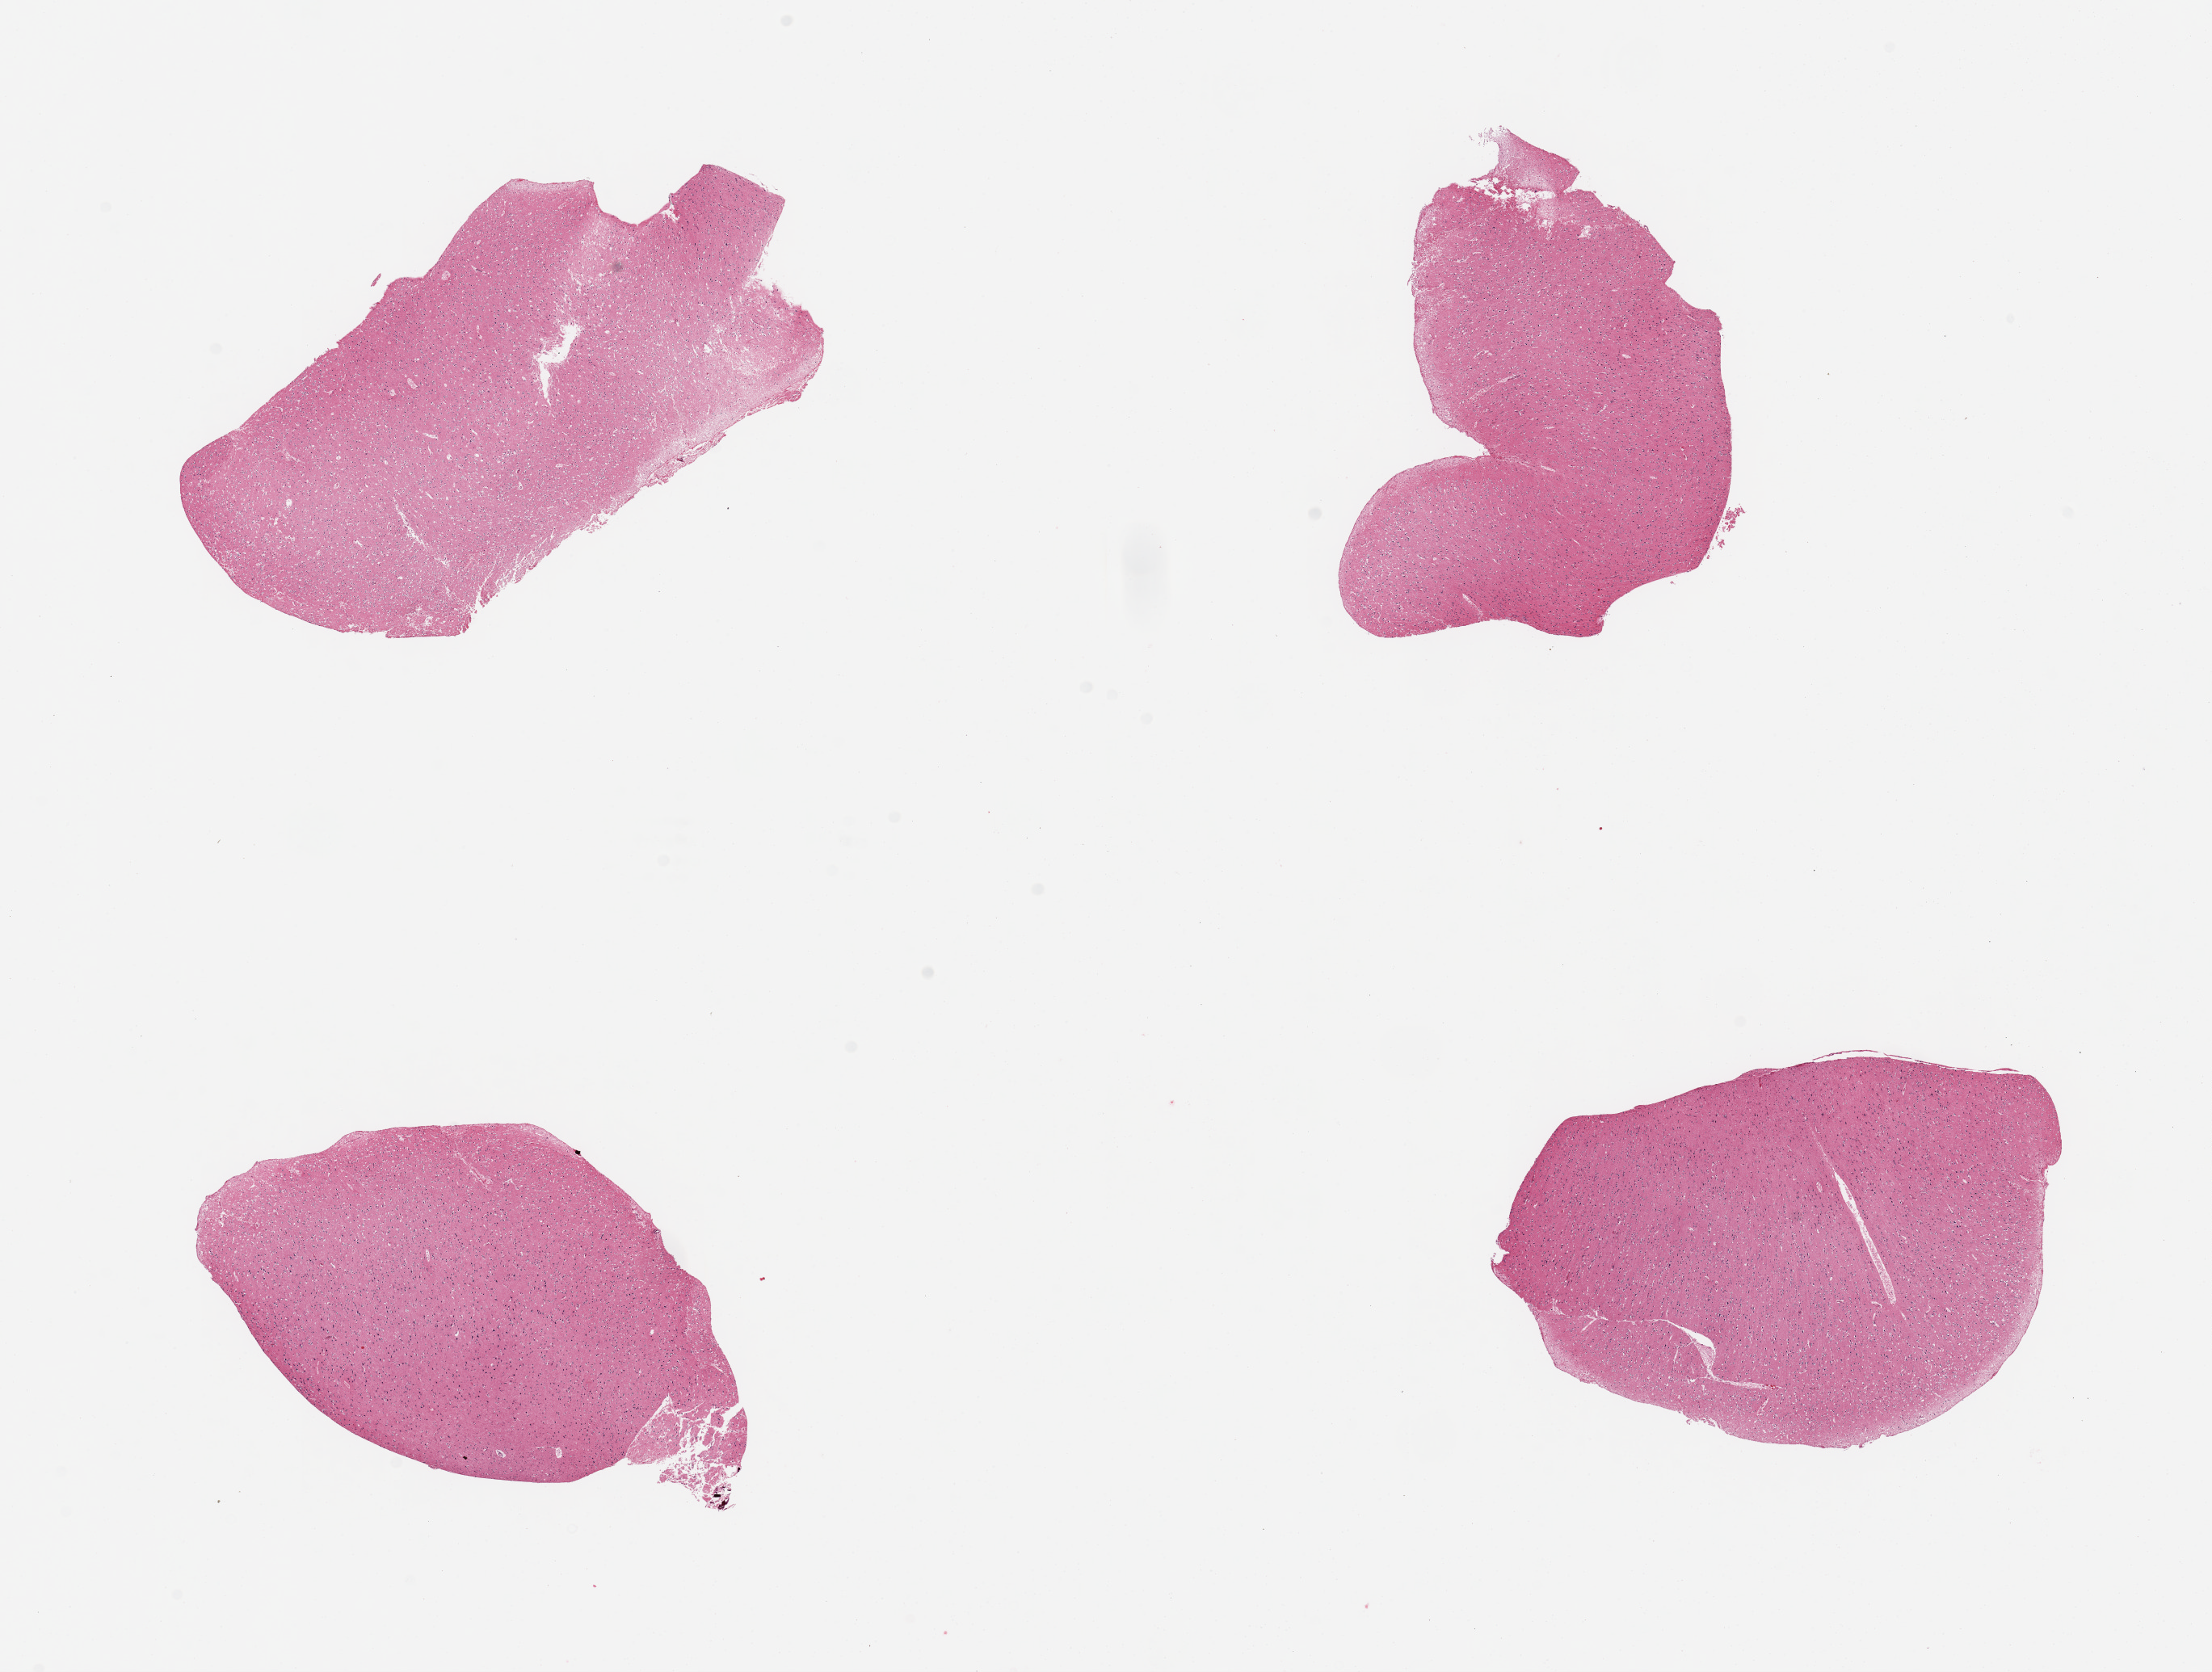
Whole-slide image, H&E stain, whole scanned area (about 21.7 x 16.4 mm, from a 20x scan) shown as a low-resolution overview. PAXgene-fixed paraffin-embedded (PFPE) section. Target tissue: cerebral cortex. Tissue donor sample.
Pathologist's review note for this sample: 4 pieces.